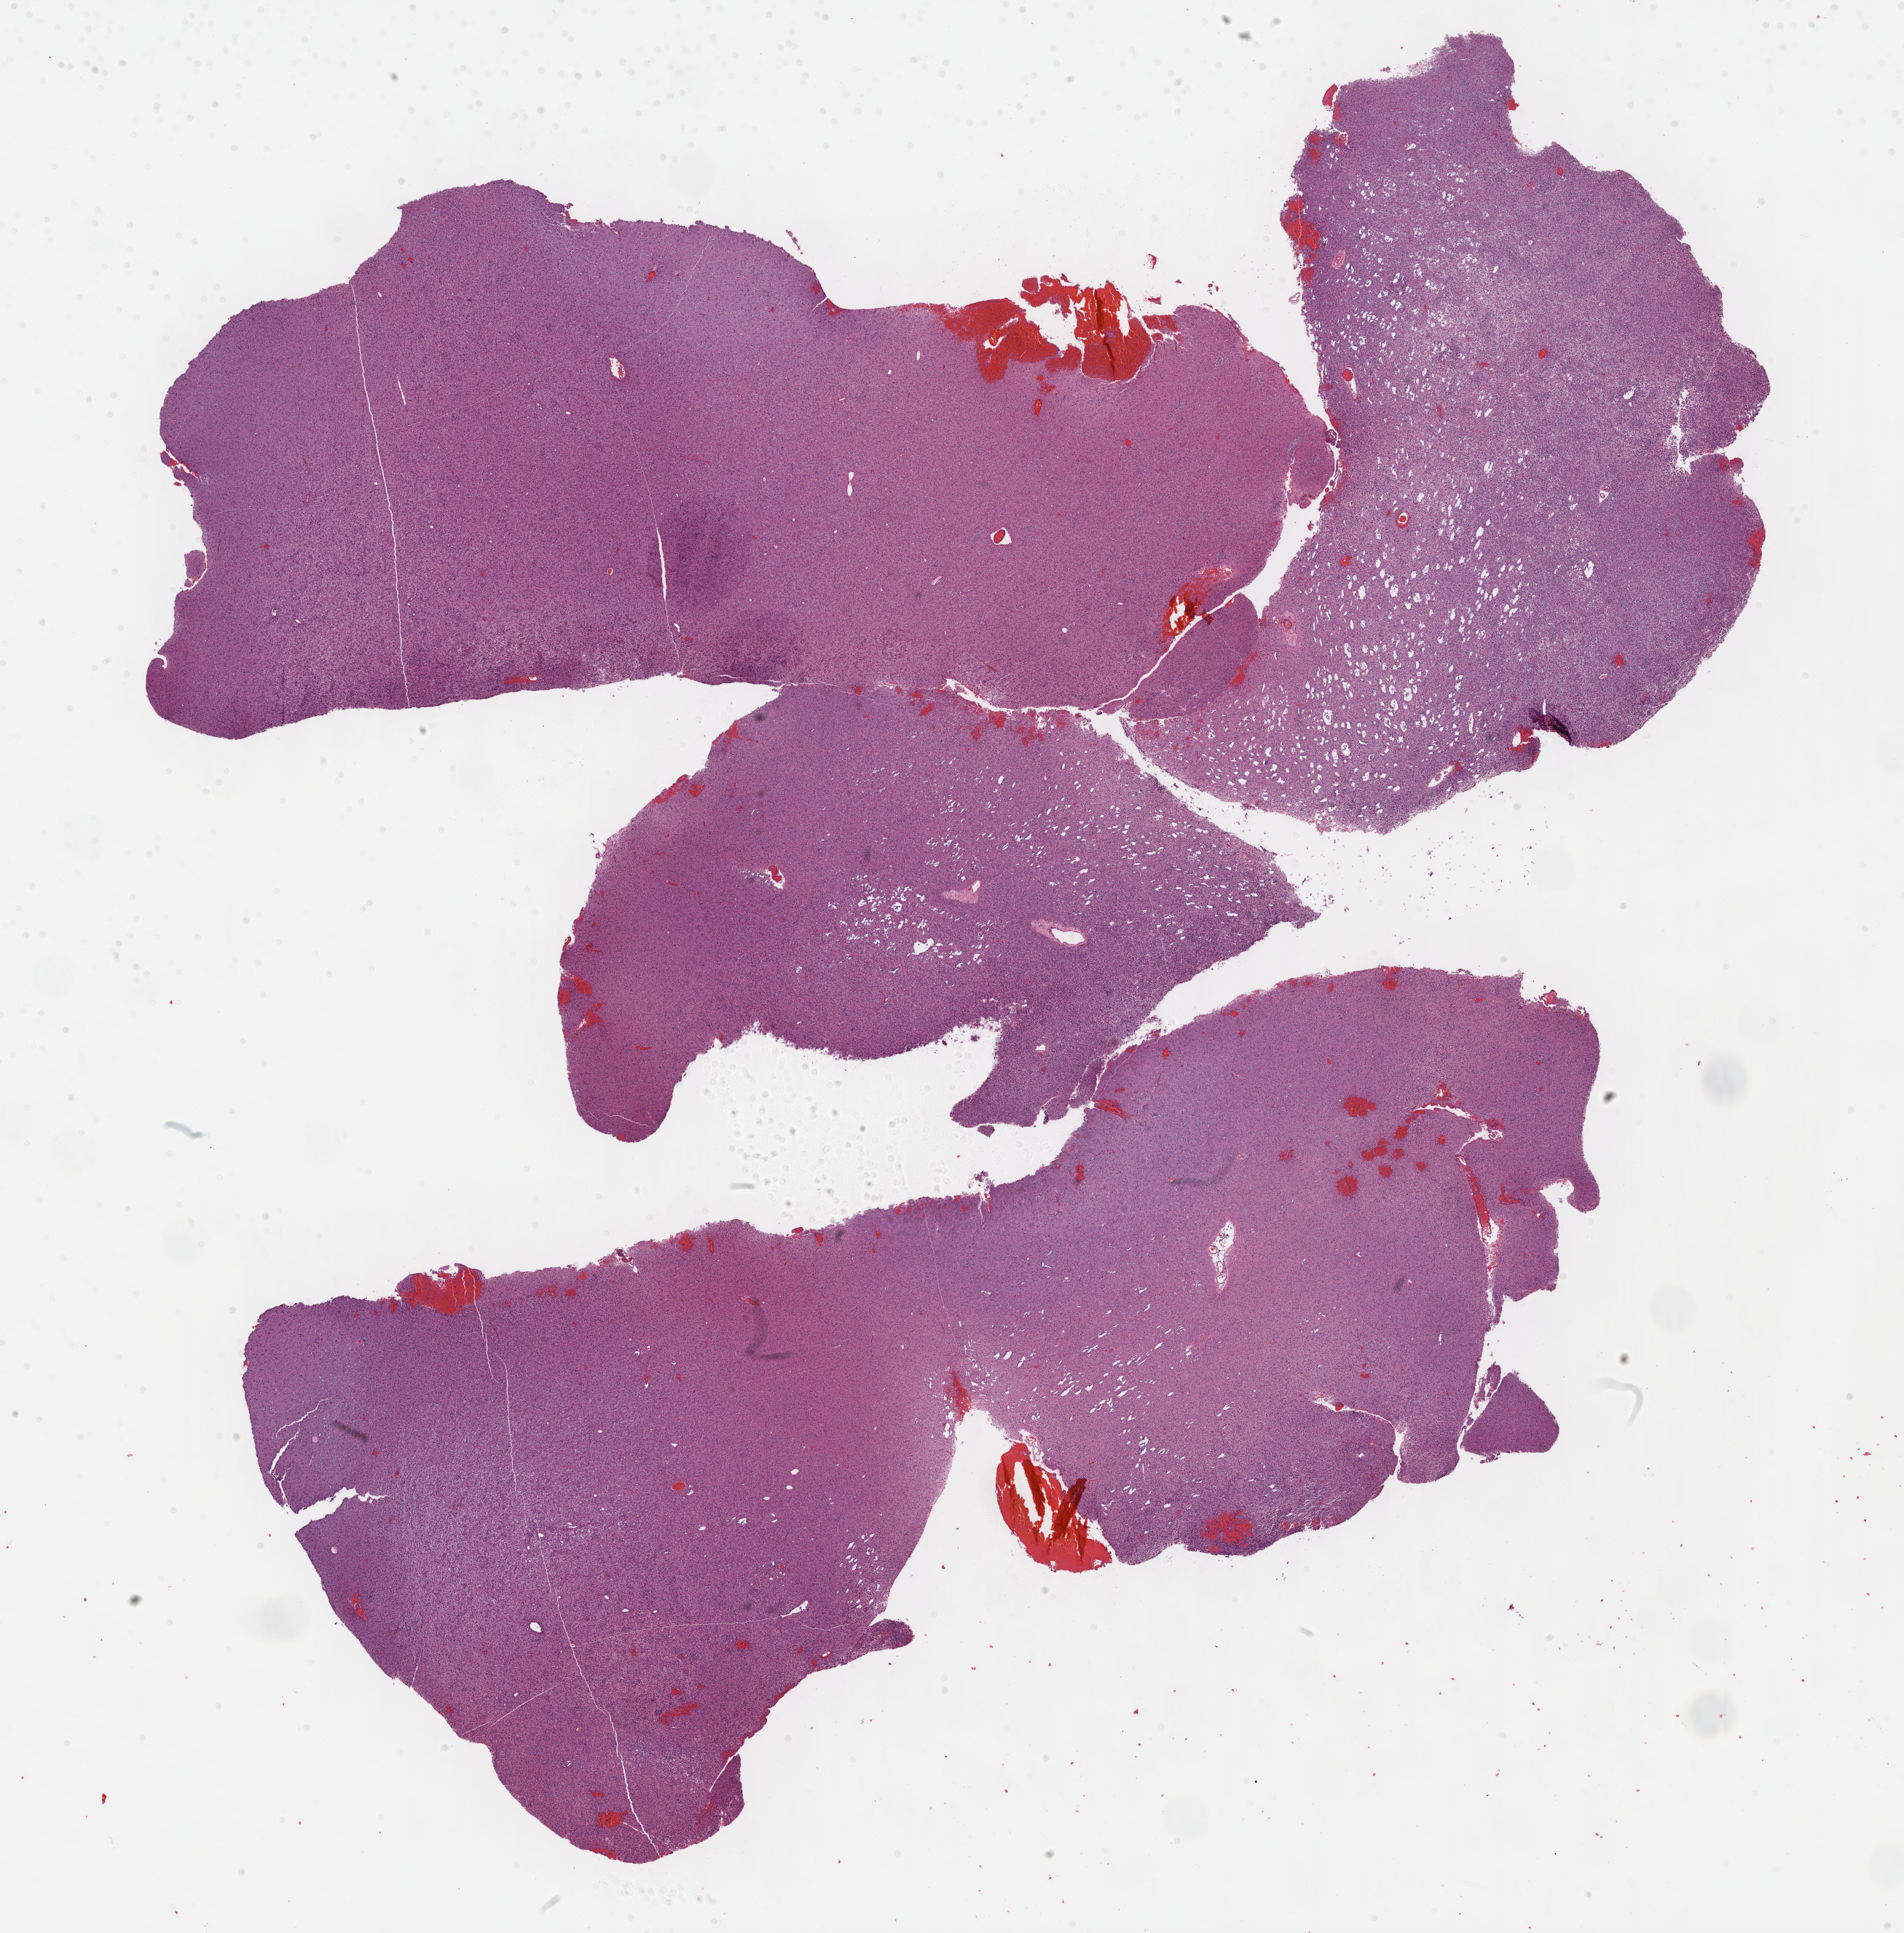
Hematoxylin and eosin (H&E) stained whole-slide image — low-resolution overview of the scanned area, about 21.1 x 21.5 mm (acquisition: 40x scan), FFPE section, brain, primary tumour sample. Patient: male, age at initial diagnosis 28 years. Histologic grade: G2 (moderately differentiated).
- laterality: right
- histologic diagnosis: Mixed glioma